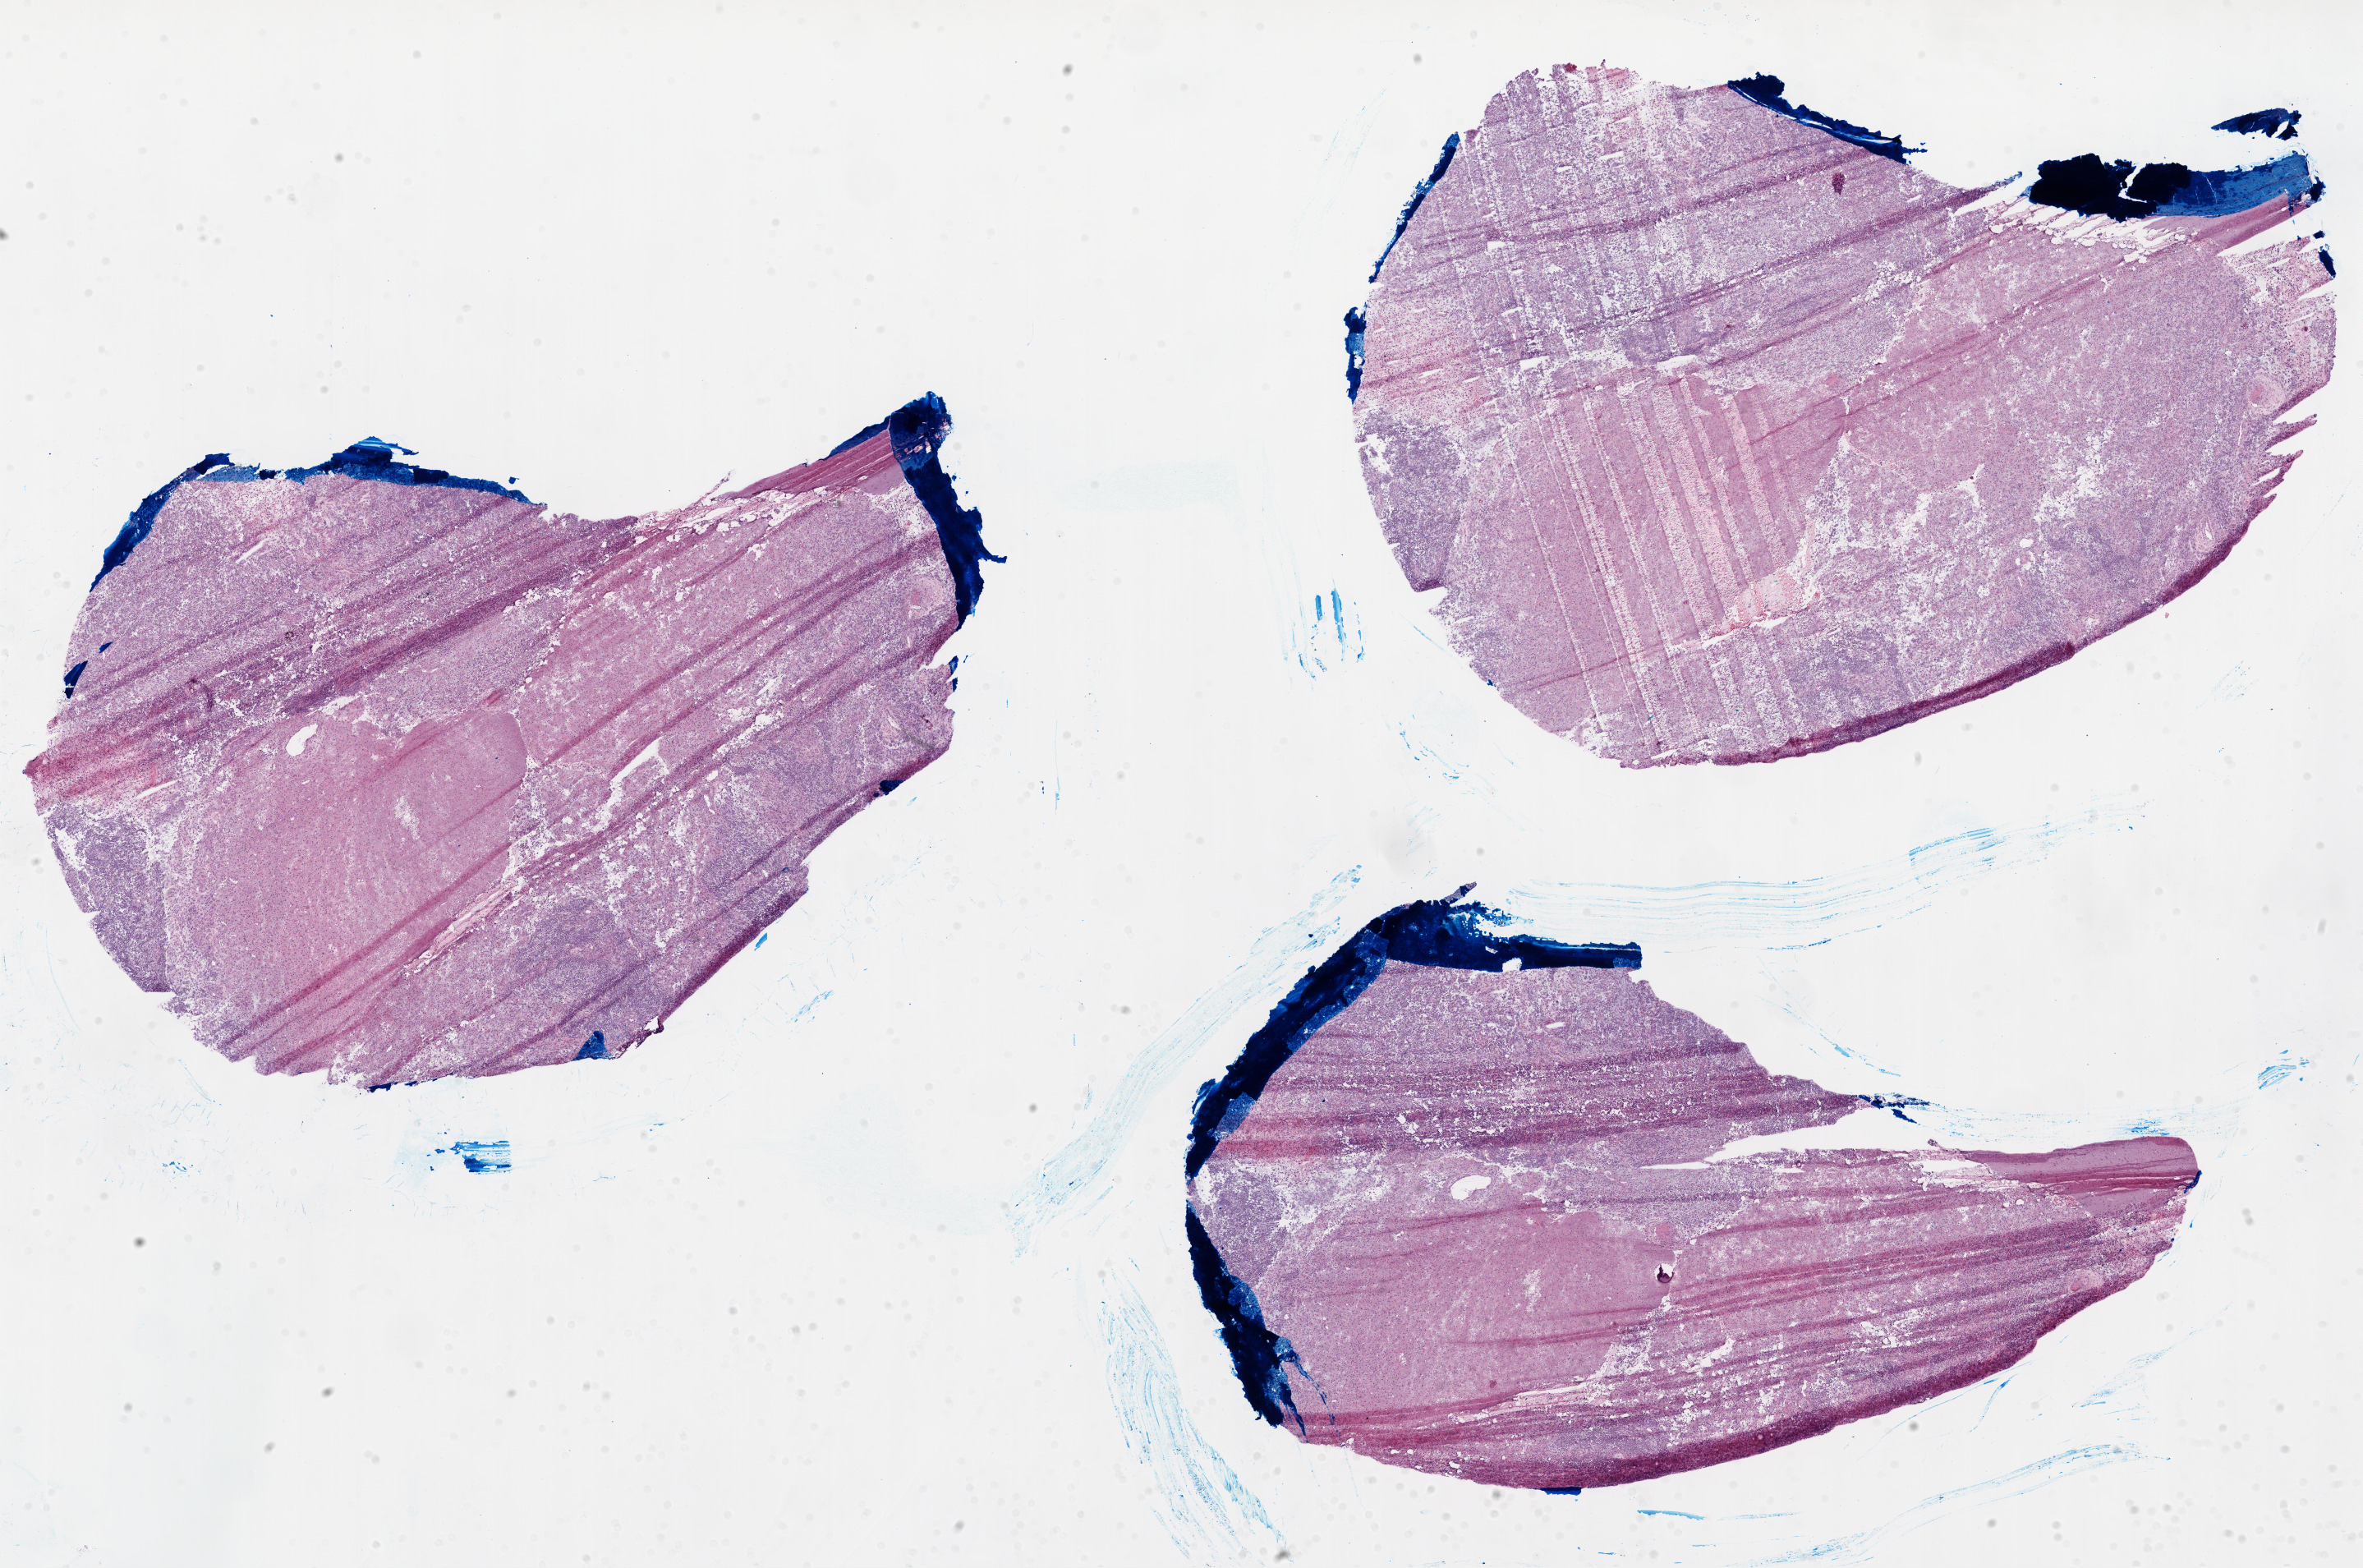
H&E whole-slide image — low-resolution overview of the scanned area, about 23.2 x 15.4 mm; frozen section from the bottom of the tissue portion; primary tumour sample from the brain. Male patient; age at initial diagnosis 64 years. Composition of this section per pathologist review: tumour cells 50%, tumour nuclei 90%, normal cells 10%, stromal cells 40%, necrosis 0%.
- histologic diagnosis: Glioblastoma